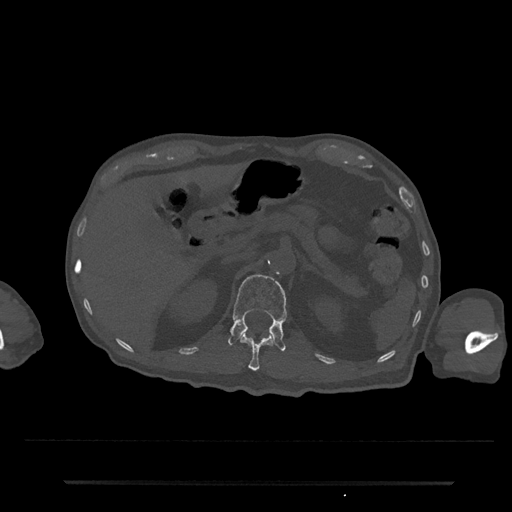
CT including the spine, one axial slice; slice 155 of 797 in the series (ordered by position); bone window (W 1800 / L 400 HU); 512 × 512 image matrix, field of view 427 × 427 mm. Male patient, age 74 years. From the clinical record (not read from this slice): primary cancer: prostate.
Structures marked on this image (semi-automatic segmentation, software-assisted and operator-edited):
- L1 vertebra: bounding box (x1, y1, x2, y2) in pixels: (228, 274, 287, 351)
- T12 vertebra: (240, 333, 273, 371)